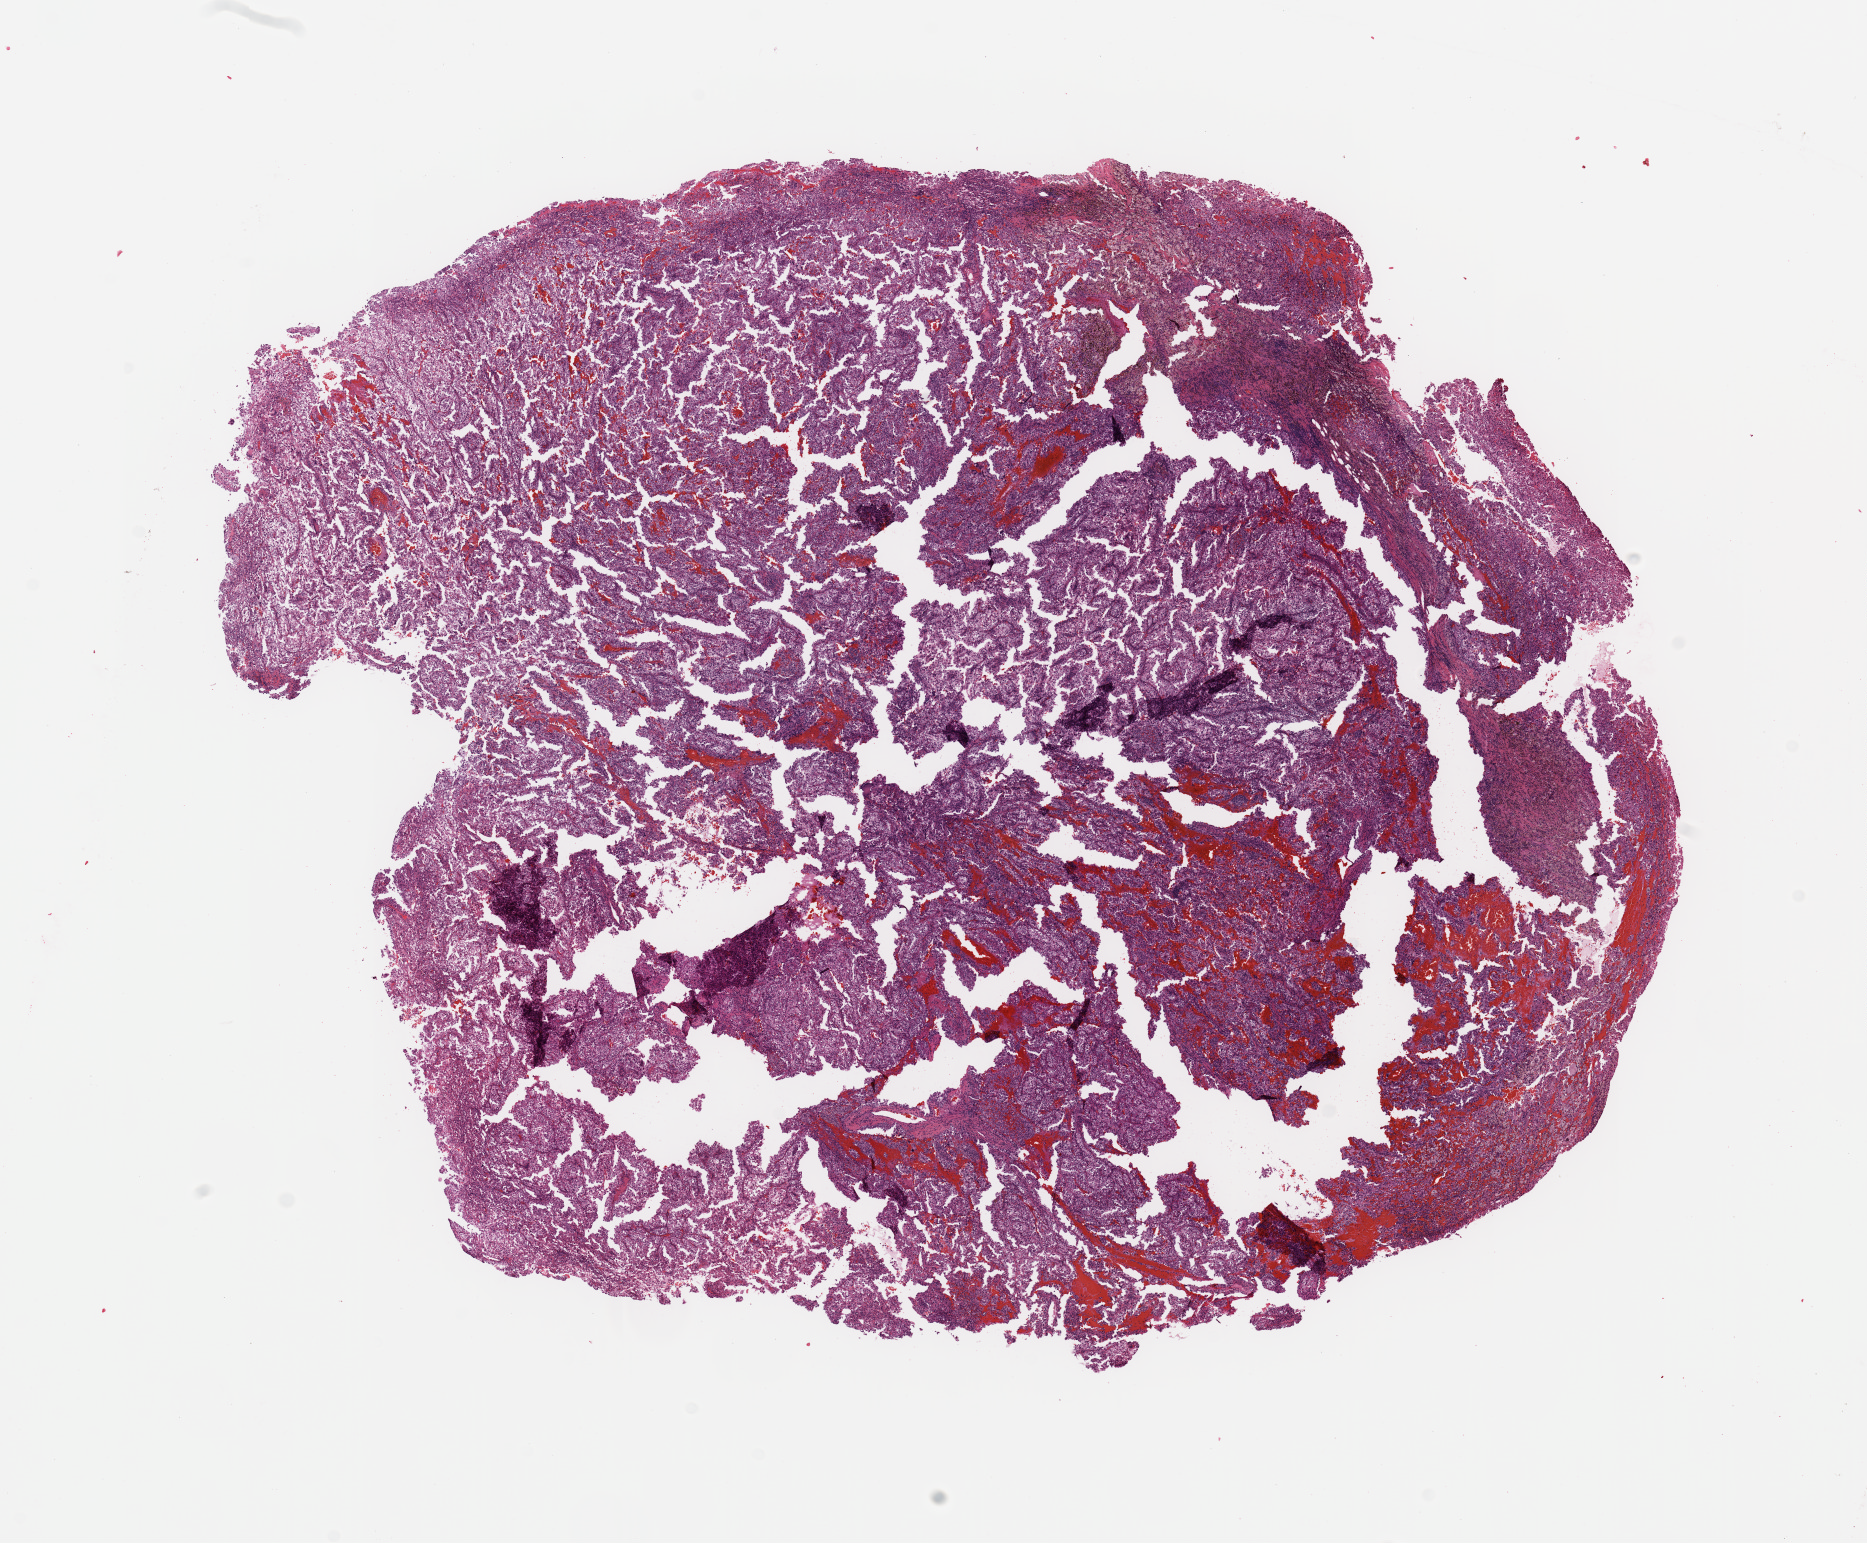
Digitized H&E tissue section (whole slide) — shown as a low-resolution overview of the whole scanned area (about 14.8 x 12.2 mm). Tumour tissue sample, sampled site: kidney. Patient: male, age 68 years. Pathologist review of this section (percent, as recorded): tumour nuclei 80%, necrosis 5%.
Diagnosis: Renal cell carcinoma, NOS.